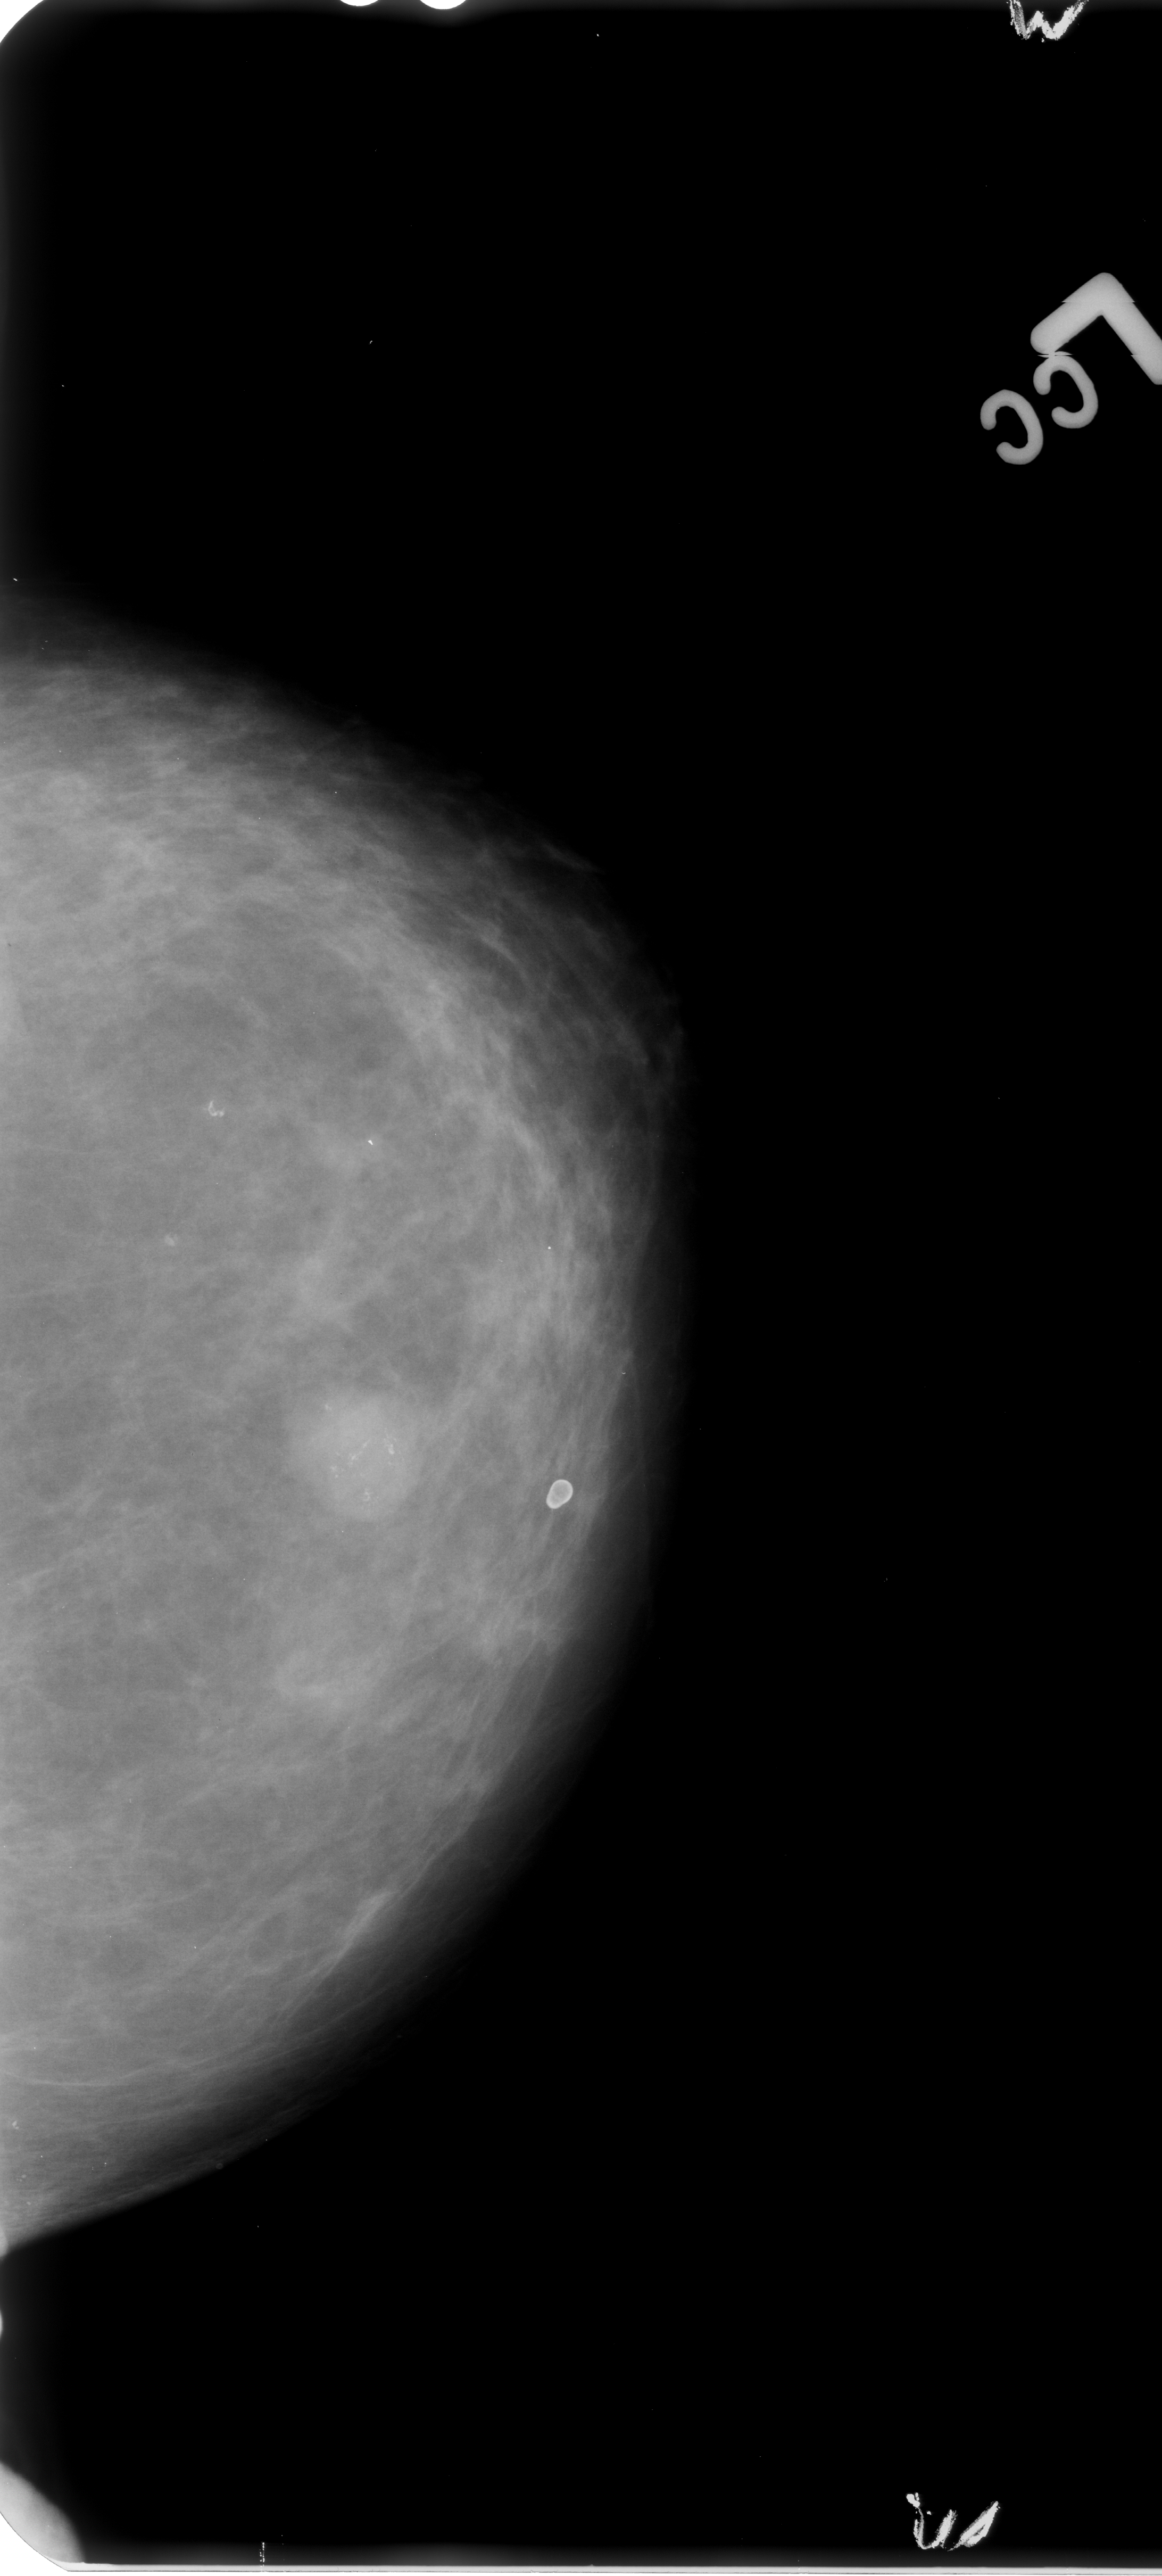
Mammogram (digitized film), left breast, craniocaudal (CC) view.
Abnormality record for this image: calcifications, morphology pleomorphic, distribution clustered; BI-RADS assessment category 4; pathology result (as recorded, not read from the image): benign.